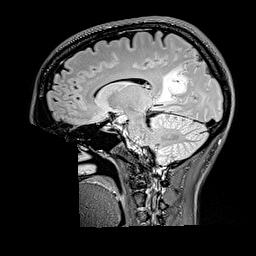
Brain MRI from a brain-tumour surgery series, one sagittal slice. Slice 98 of 176 in the series (ordered by position). T2 FLAIR. 1 mm slice thickness. 256 × 256 image matrix, field of view 256 × 256 mm. From the clinical record (not read from this slice): histopathology: Oligodendroglioma; WHO grade: 2; IDH mutation: yes.
Outlined on this slice (outlined manually by an expert reader):
- tumour: bounding box <160,66,188,104> (left, top, right, bottom; pixels)